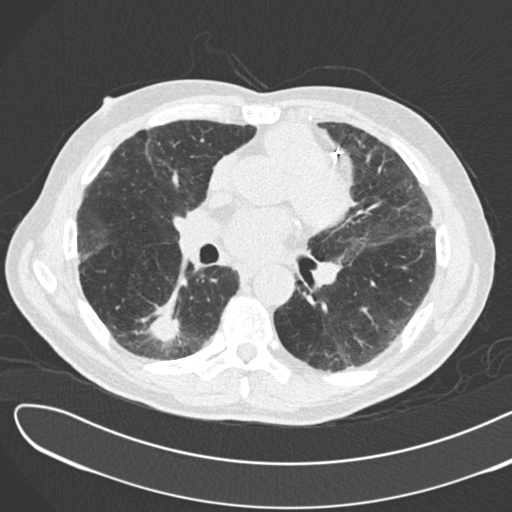
Low-dose screening chest CT, axial slice. Second screening round (one year after baseline). Lung window (W 1500 / L -600 HU). 120 kVp. Slice 96 of 183 in the series. 512 × 512 image matrix, field of view 370 × 370 mm. Male participant, aged 72 years at enrolment. Former smoker at enrolment.
Lesion marked by an expert reader, bounding box [x1, y1, x2, y2] px = [131, 291, 195, 352]. The screening reader recorded 2 non-calcified nodules or masses ≥4 mm on this exam (right lower lobe, right lower lobe); which of them this box marks is not recorded. Official screen result: positive, change unspecified: nodule(s) >= 4 mm or enlarging nodule(s), mass(es), or other non-specific abnormalities suspicious for lung cancer. Later outcome: lung cancer diagnosed 46 days after this screen — squamous cell carcinoma, NOS, right lower lobe, poorly differentiated (G3), stage IB (AJCC 6th edition), 42 mm at pathology.